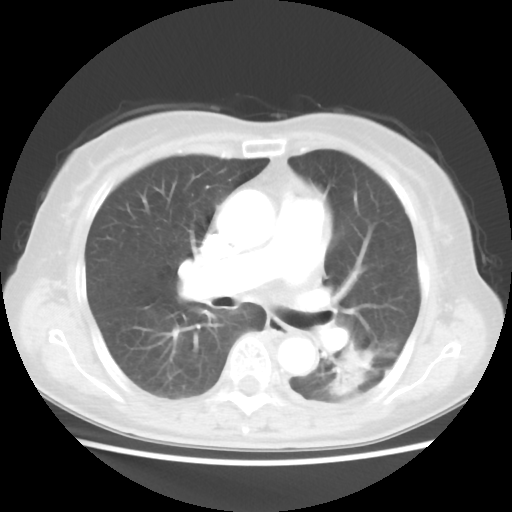
Chest CT, one axial slice. Slice 21 of 40 in the series (ordered by position). Lung window (W 1500 / L -600 HU). 5 mm slice thickness. 512 × 512 image matrix. Female patient, age 69 years. From the clinical record (not read from this slice): clinical TNM (as recorded): T1c N0 M0.
Structures marked on this image (bounding box drawn by a radiologist):
- lung tumour (recorded histology: adenocarcinoma): bounding box [x1, y1, x2, y2] px = [334, 343, 372, 398]